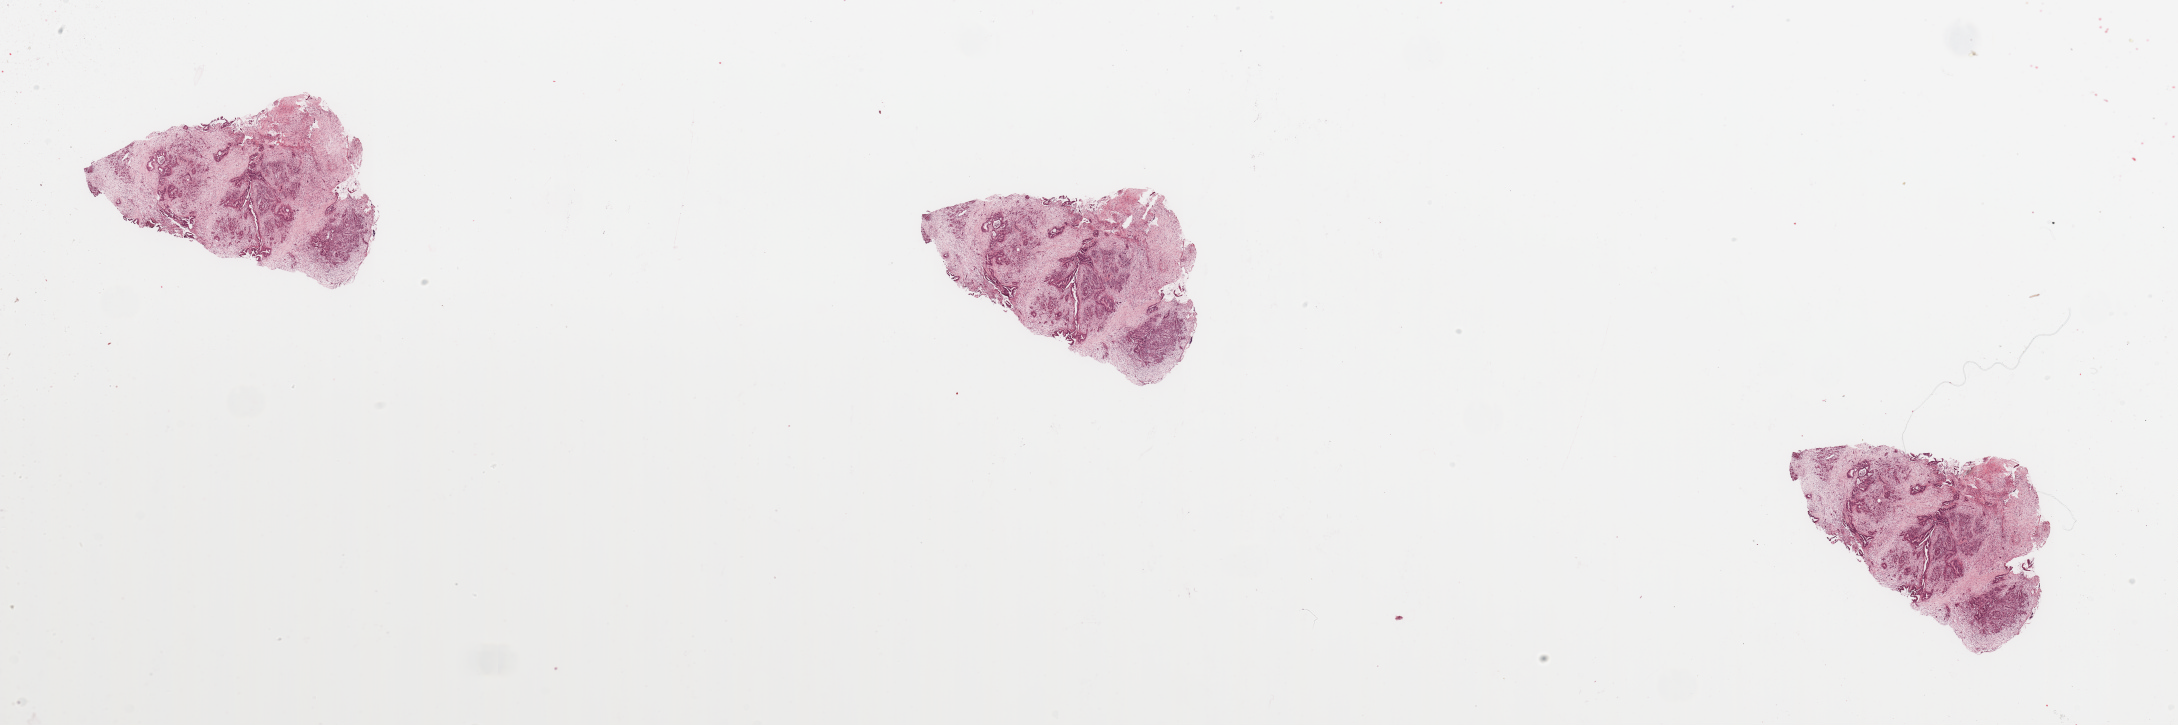
Digitized H&E tissue section (whole slide), shown as a low-resolution overview of the whole scanned area (about 34.5 x 11.5 mm, from a 20x scan), tumour tissue sample, sampled site: pancreas. 54-year-old female patient. Histologic grade: G2 (moderately differentiated). Pathologist review of this section (percent, as recorded): tumour nuclei 20%, necrosis 0%.
AJCC pathologic stage: IB. Diagnosis: Infiltrating duct carcinoma, NOS. Primary tumour site (as recorded): head.